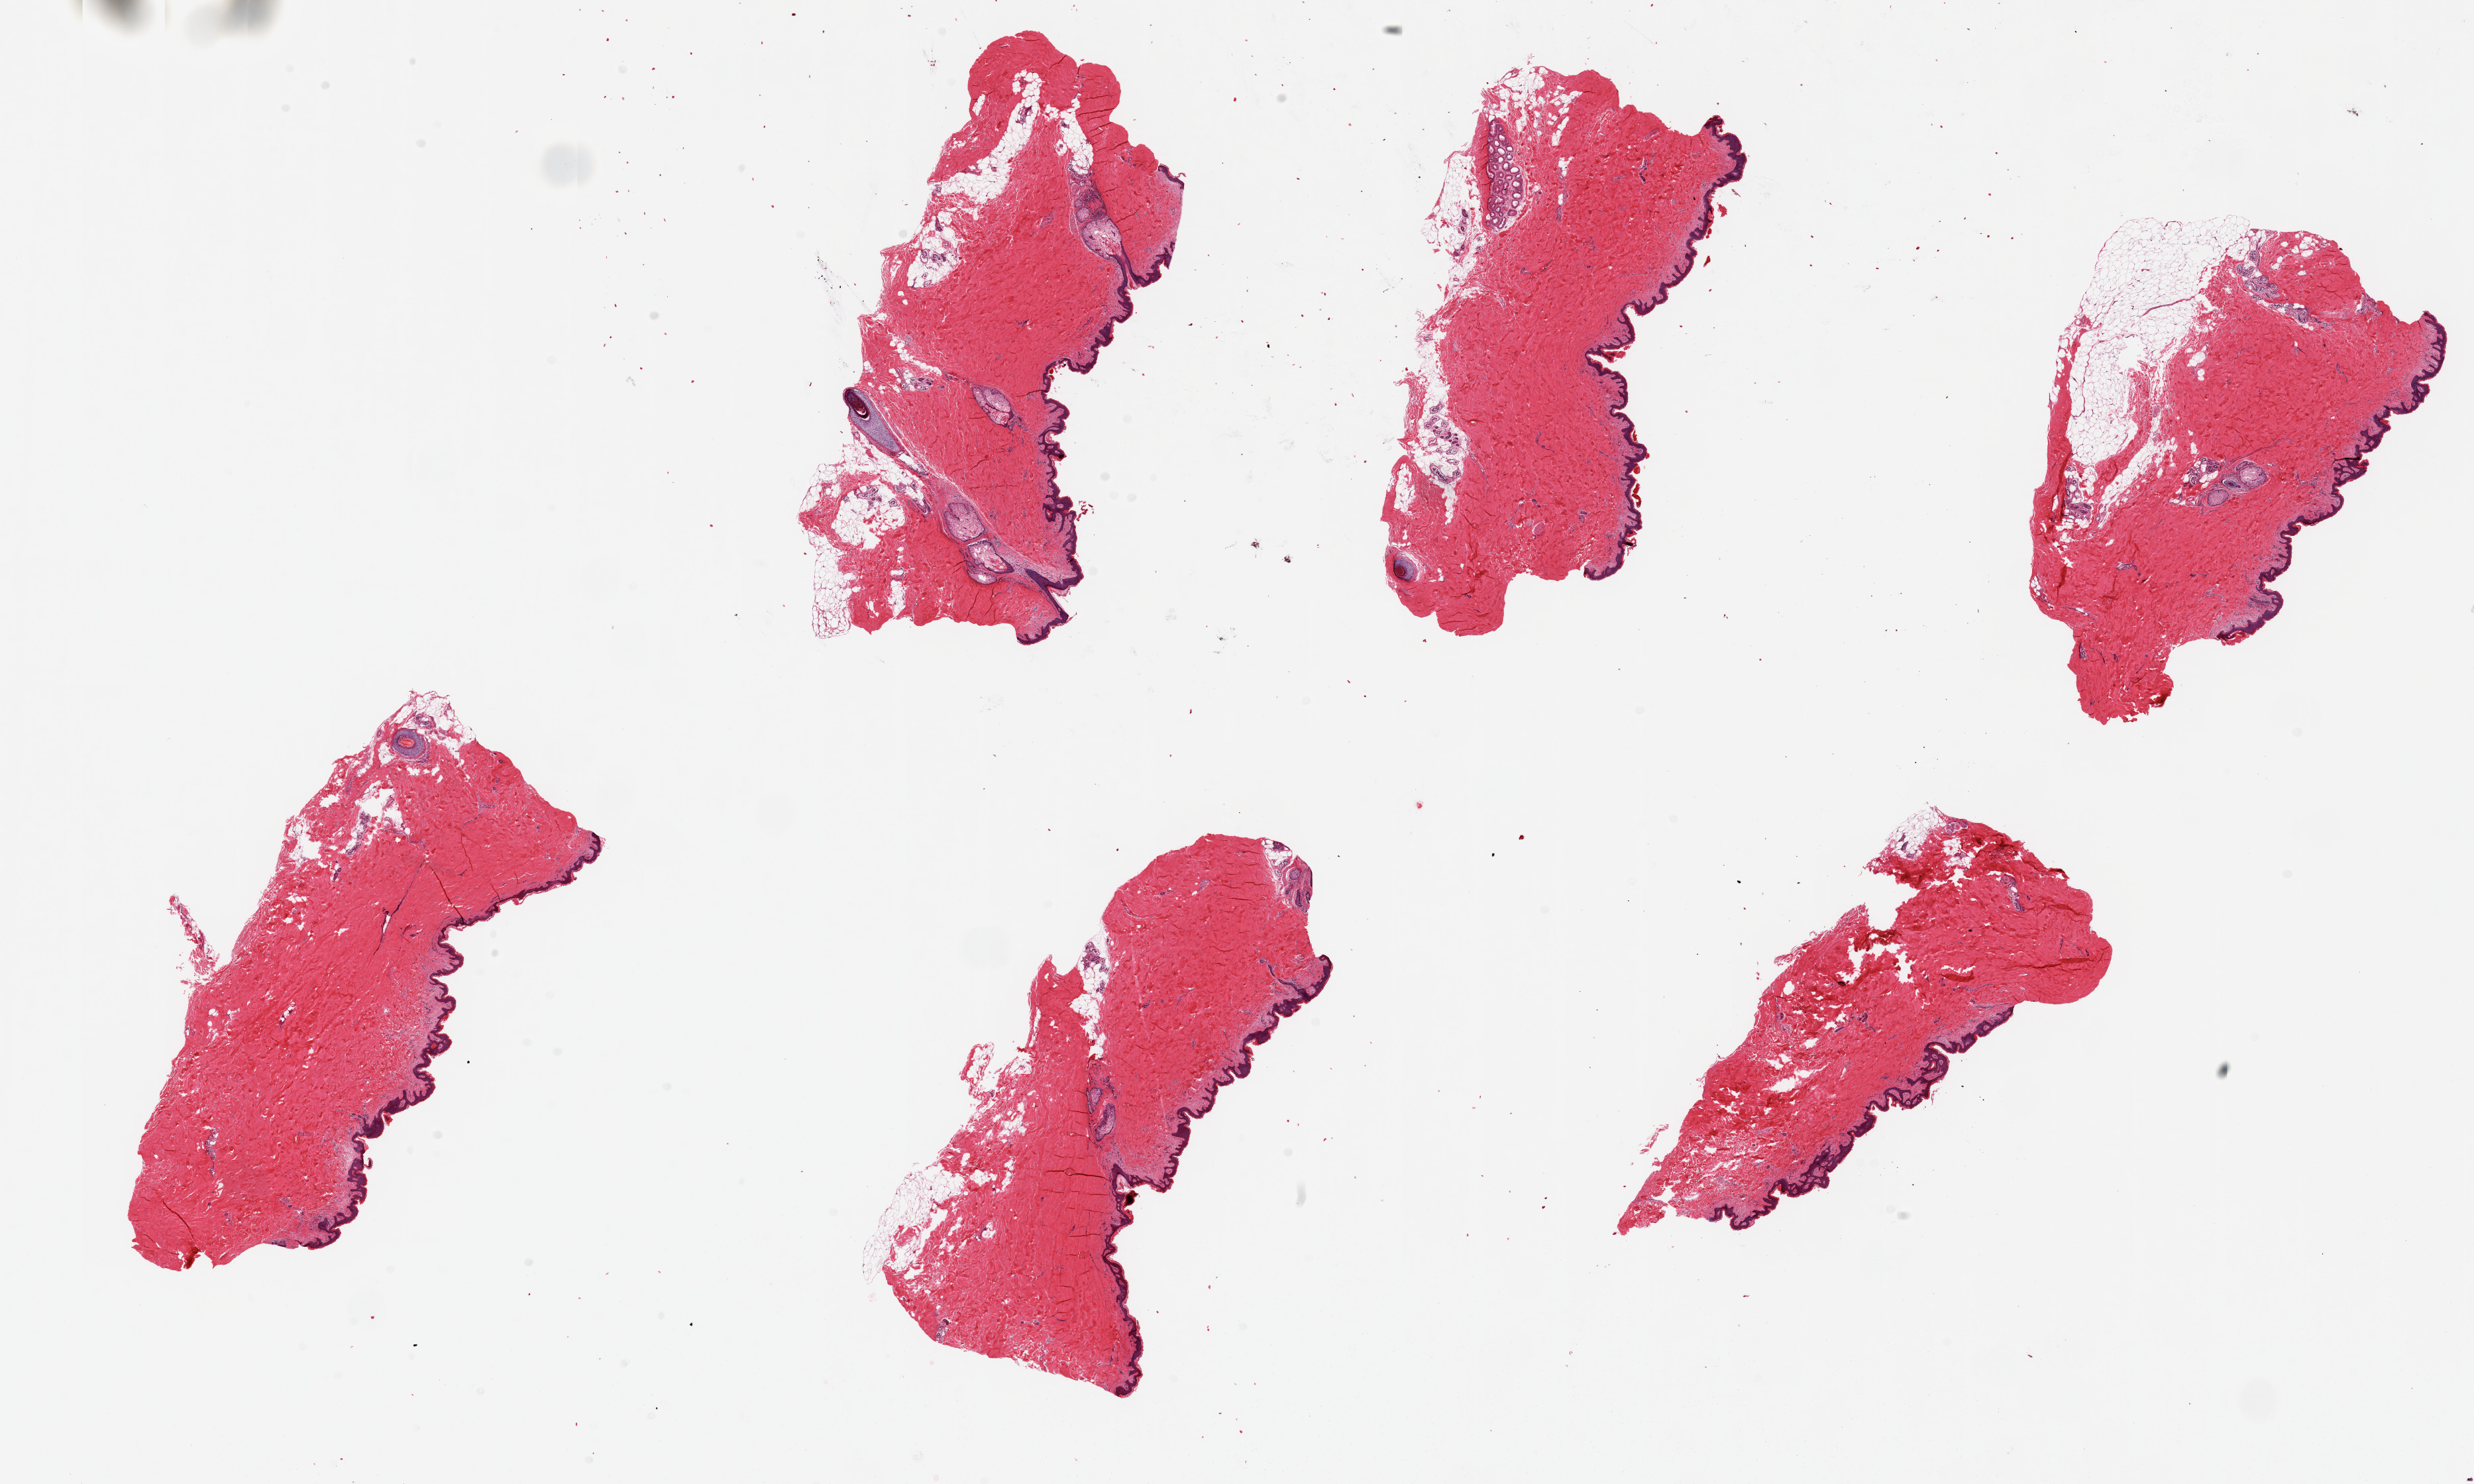
Digitized H&E-stained section — shown as a low-resolution overview of the whole scanned area (about 29.5 x 17.7 mm). PAXgene-fixed paraffin-embedded (PFPE) section. Target tissue: skin of suprapubic region. Donor tissue sample. Male donor.
* review note (as recorded): 6 pieces, up to 8x3mm; subcutaneous adipose is up to 1 mm thick in 2 pieces